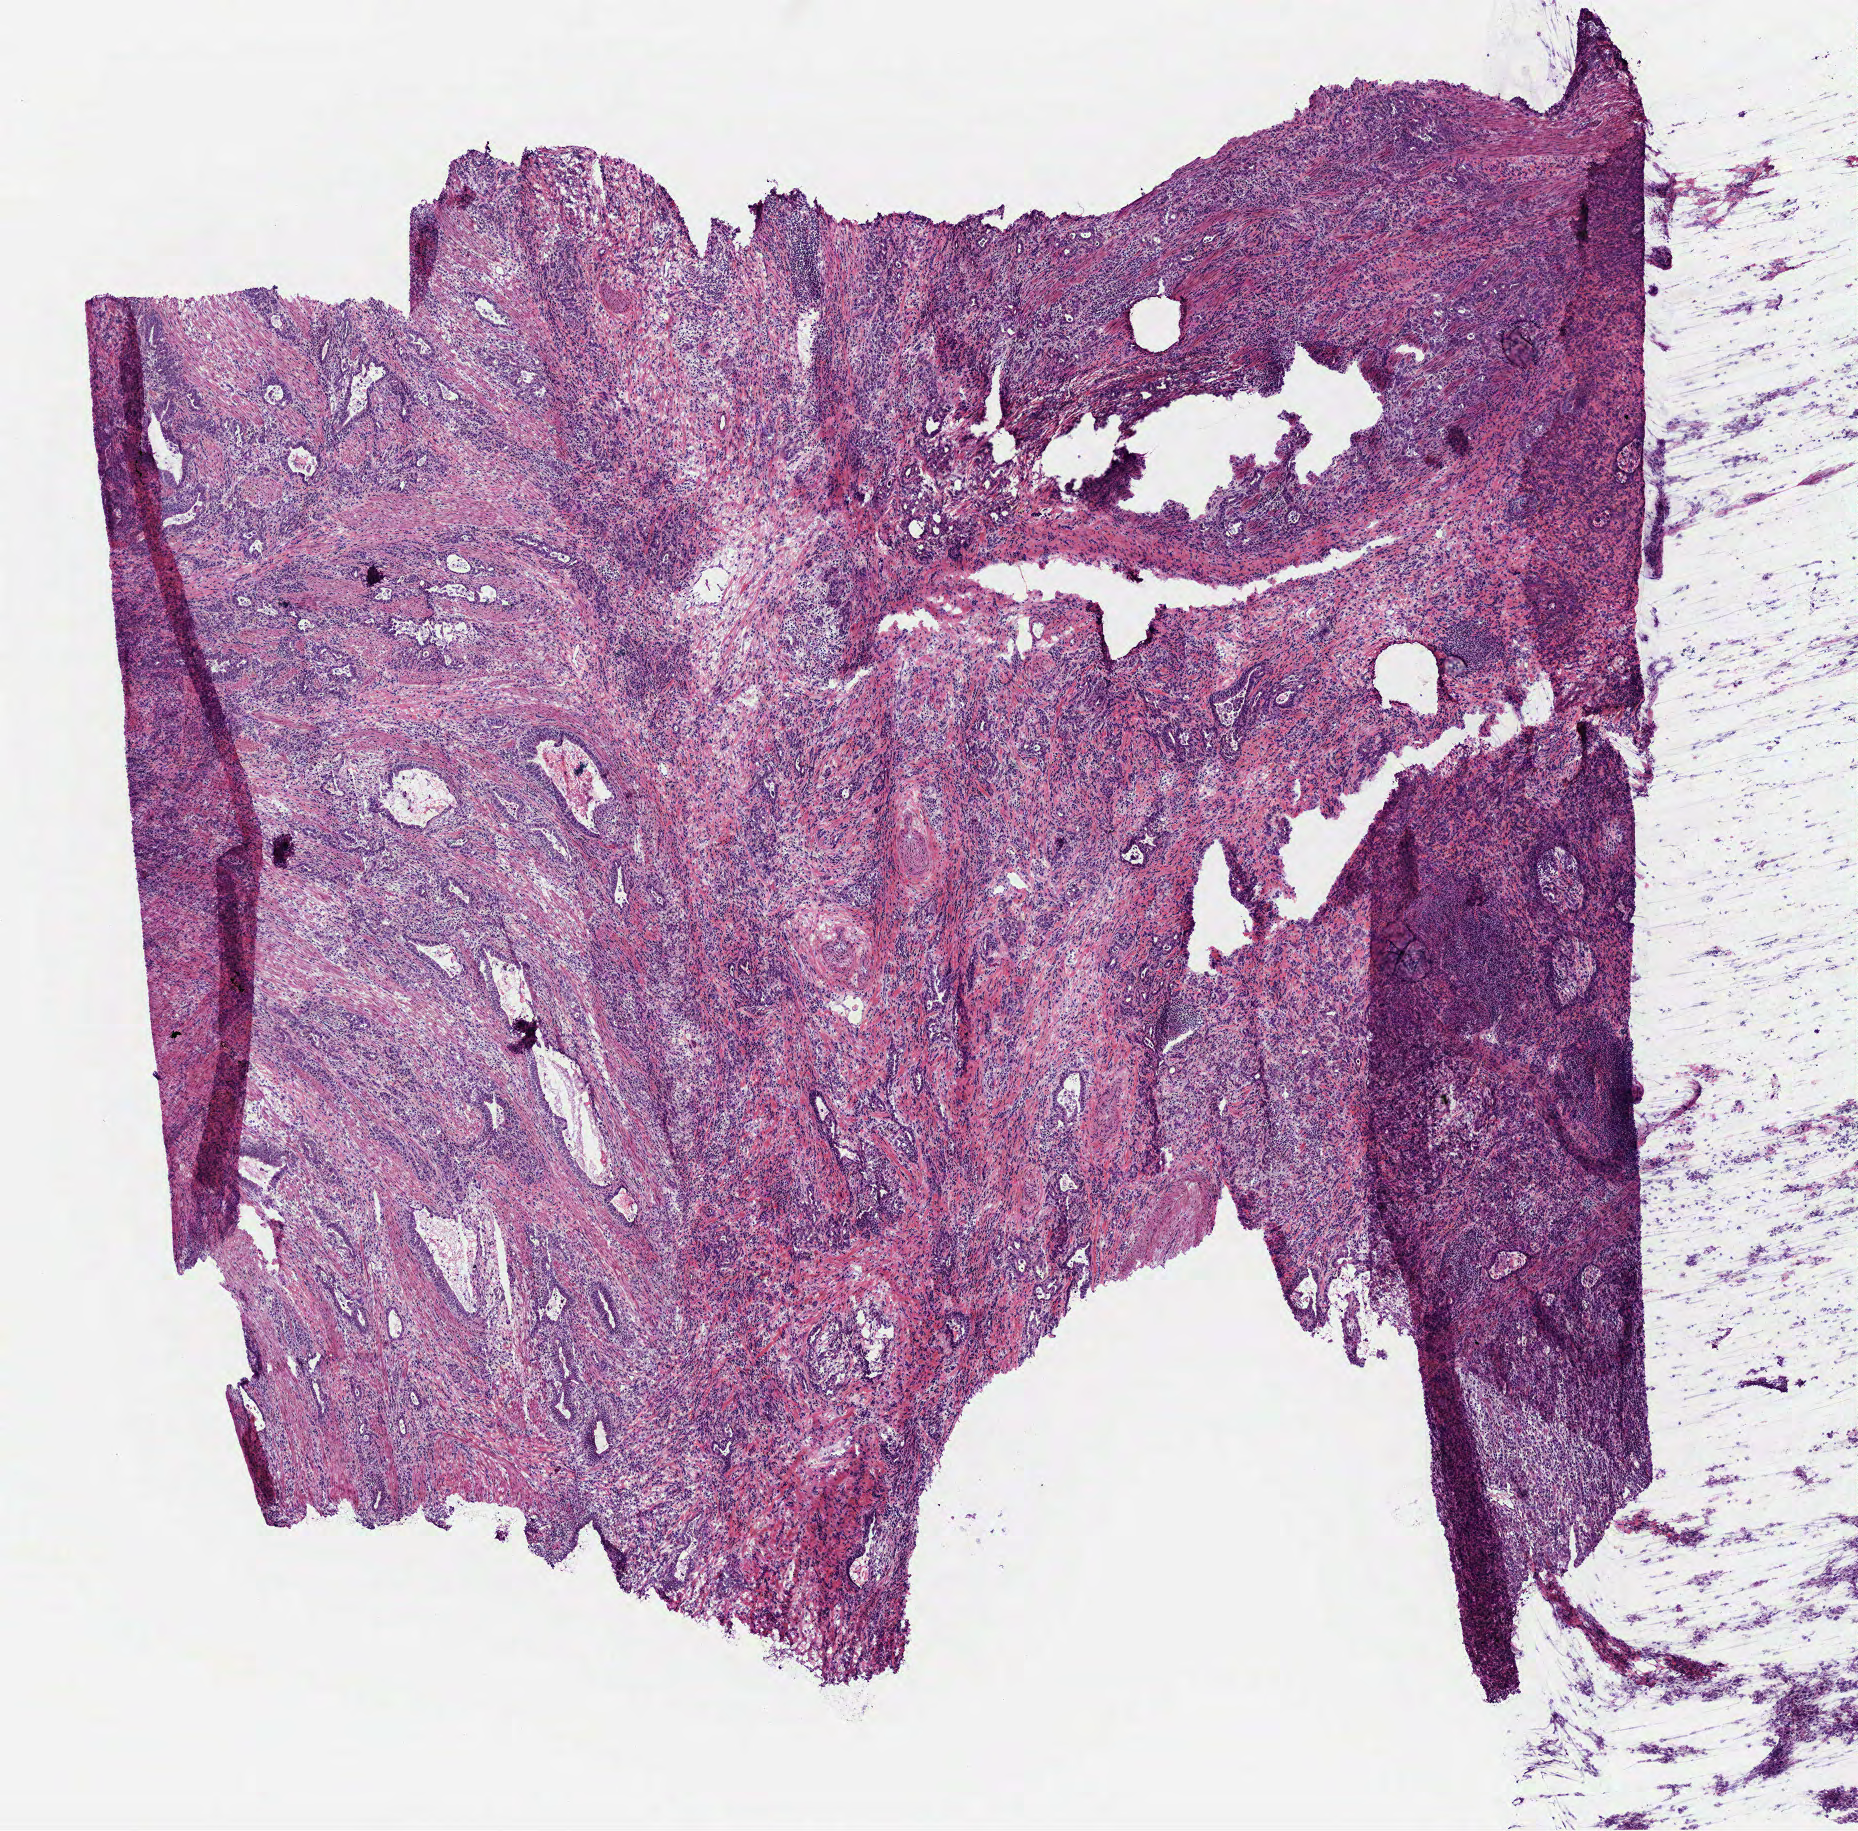
Hematoxylin and eosin (H&E) stained whole-slide image — shown as a low-resolution overview of the whole scanned area (about 7.5 x 7.4 mm, from a 40x scan), frozen section from the bottom of the tissue portion, primary tumour sample from the stomach. Male, age 77 years at initial diagnosis. Histologic grade: G3 (poorly differentiated). Composition of this section per pathologist review: tumour cells 70%, tumour nuclei 45%, normal cells 0%, stromal cells 30%, necrosis 0%.
Pathologic diagnosis: Carcinoma, diffuse type (gastric antrum). Lymph nodes positive (case pathology): 10 of 20 examined. AJCC pathologic stage: IIIC (7th edition).